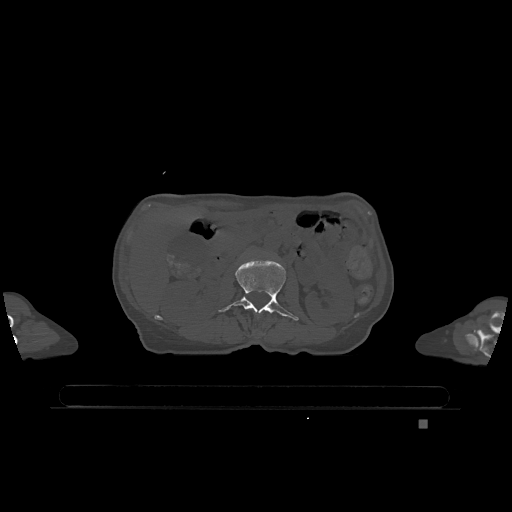
CT including the spine, one axial slice. Position 415 of 1317 along the scan axis. Bone window (W 1800 / L 400 HU). 512 × 512 image matrix. Patient: female, 74 years. Case-level facts recorded for this patient, not image findings: primary cancer: lung.
Annotated regions visible in this slice (semi-automatic segmentation, software-assisted and operator-edited):
- L2 vertebra: bounding box <218,259,299,321> (left, top, right, bottom; pixels)